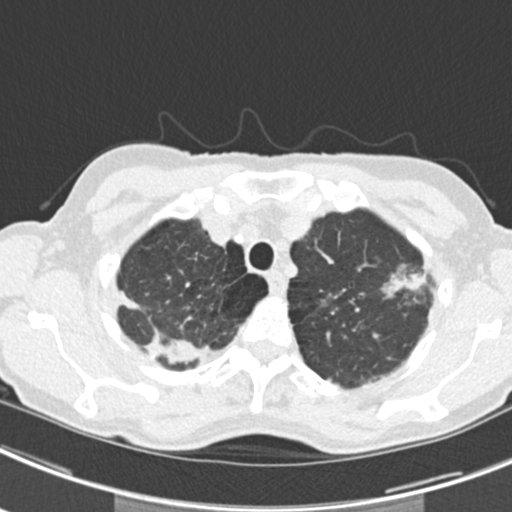
Low-dose screening chest CT, axial slice. Second screening round (one year after baseline). Lung window (W 1500 / L -600 HU). 120 kVp. Slice 37 of 219 in the series. 512 × 512 image matrix, field of view 298 × 298 mm. Female, age 63 years at enrolment. Current smoker at enrolment.
Lesion marked by an expert reader, bounding box (x1, y1, x2, y2) in pixels: (373, 251, 437, 312). The screening reader recorded 9 non-calcified nodules or masses ≥4 mm on this exam (left upper lobe, right upper lobe, left upper lobe, left lower lobe, right middle lobe, left lower lobe, left lower lobe, right lower lobe, right lower lobe); which of them this box marks is not recorded. Official screen result: positive, other. Lung cancer was diagnosed 408 days after this screen (after the third annual screen): bronchiolo-alveolar adenocarcinoma, NOS, right upper lobe, right middle lobe, right lower lobe, left upper lobe, left lower lobe, moderately differentiated (G2), stage IV (AJCC 6th edition).